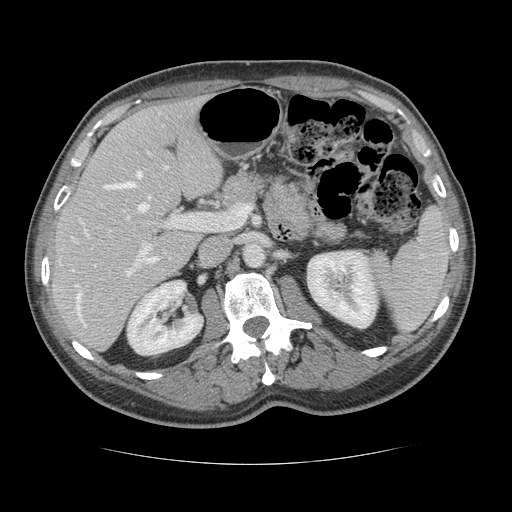
Contrast-enhanced abdominal CT, one axial slice; slice 73 of 134 in the series (ordered by position); intravenous contrast given; soft-tissue window (W 400 / L 40 HU); 2.5 mm slice thickness; 512 × 512 image matrix. Male patient, age 68 years. From the clinical record (not read from this slice): diagnosis: colorectal cancer liver metastases, imaged before liver resection; multiple liver metastases: yes.
Annotated regions visible in this slice (outlined manually by an expert reader):
- hepatic veins: bounding box (x1, y1, x2, y2) in pixels: (76, 171, 151, 326)
- liver: (52, 100, 222, 350)
- planned liver remnant (the part of the liver to remain after resection): (52, 100, 222, 337)
- portal vein (with intrahepatic branches): (127, 216, 196, 275)